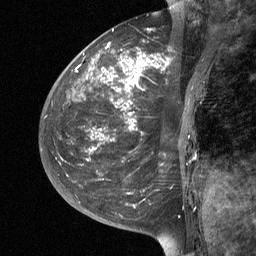
Breast MRI (dynamic contrast-enhanced), one sagittal slice. Slice 17 of 64 in the series (ordered by position). Dynamic contrast-enhanced study with each time point stored as its own series, time point 2 of 3 at this slice position (early post-contrast, ordered by acquisition time). 1.5 T. TE 4.8 ms, TR 27 ms. 256 × 256 image matrix, field of view 200 × 200 mm. Patient: female, 42 years. From the clinical record (not read from this slice): setting: breast cancer imaged before/during neoadjuvant chemotherapy; receptor status: triple-negative.
Annotated regions visible in this slice (semi-automatic segmentation, software-assisted and operator-edited):
- analysis volume of interest (the breast-tissue region the enhancement analysis was run in; not a lesion): bounding box <43,29,203,190> (left, top, right, bottom; pixels)
- tumour enhancement mask (voxels above the 90 % enhancement threshold inside the analysis volume of interest): <79,43,158,151>